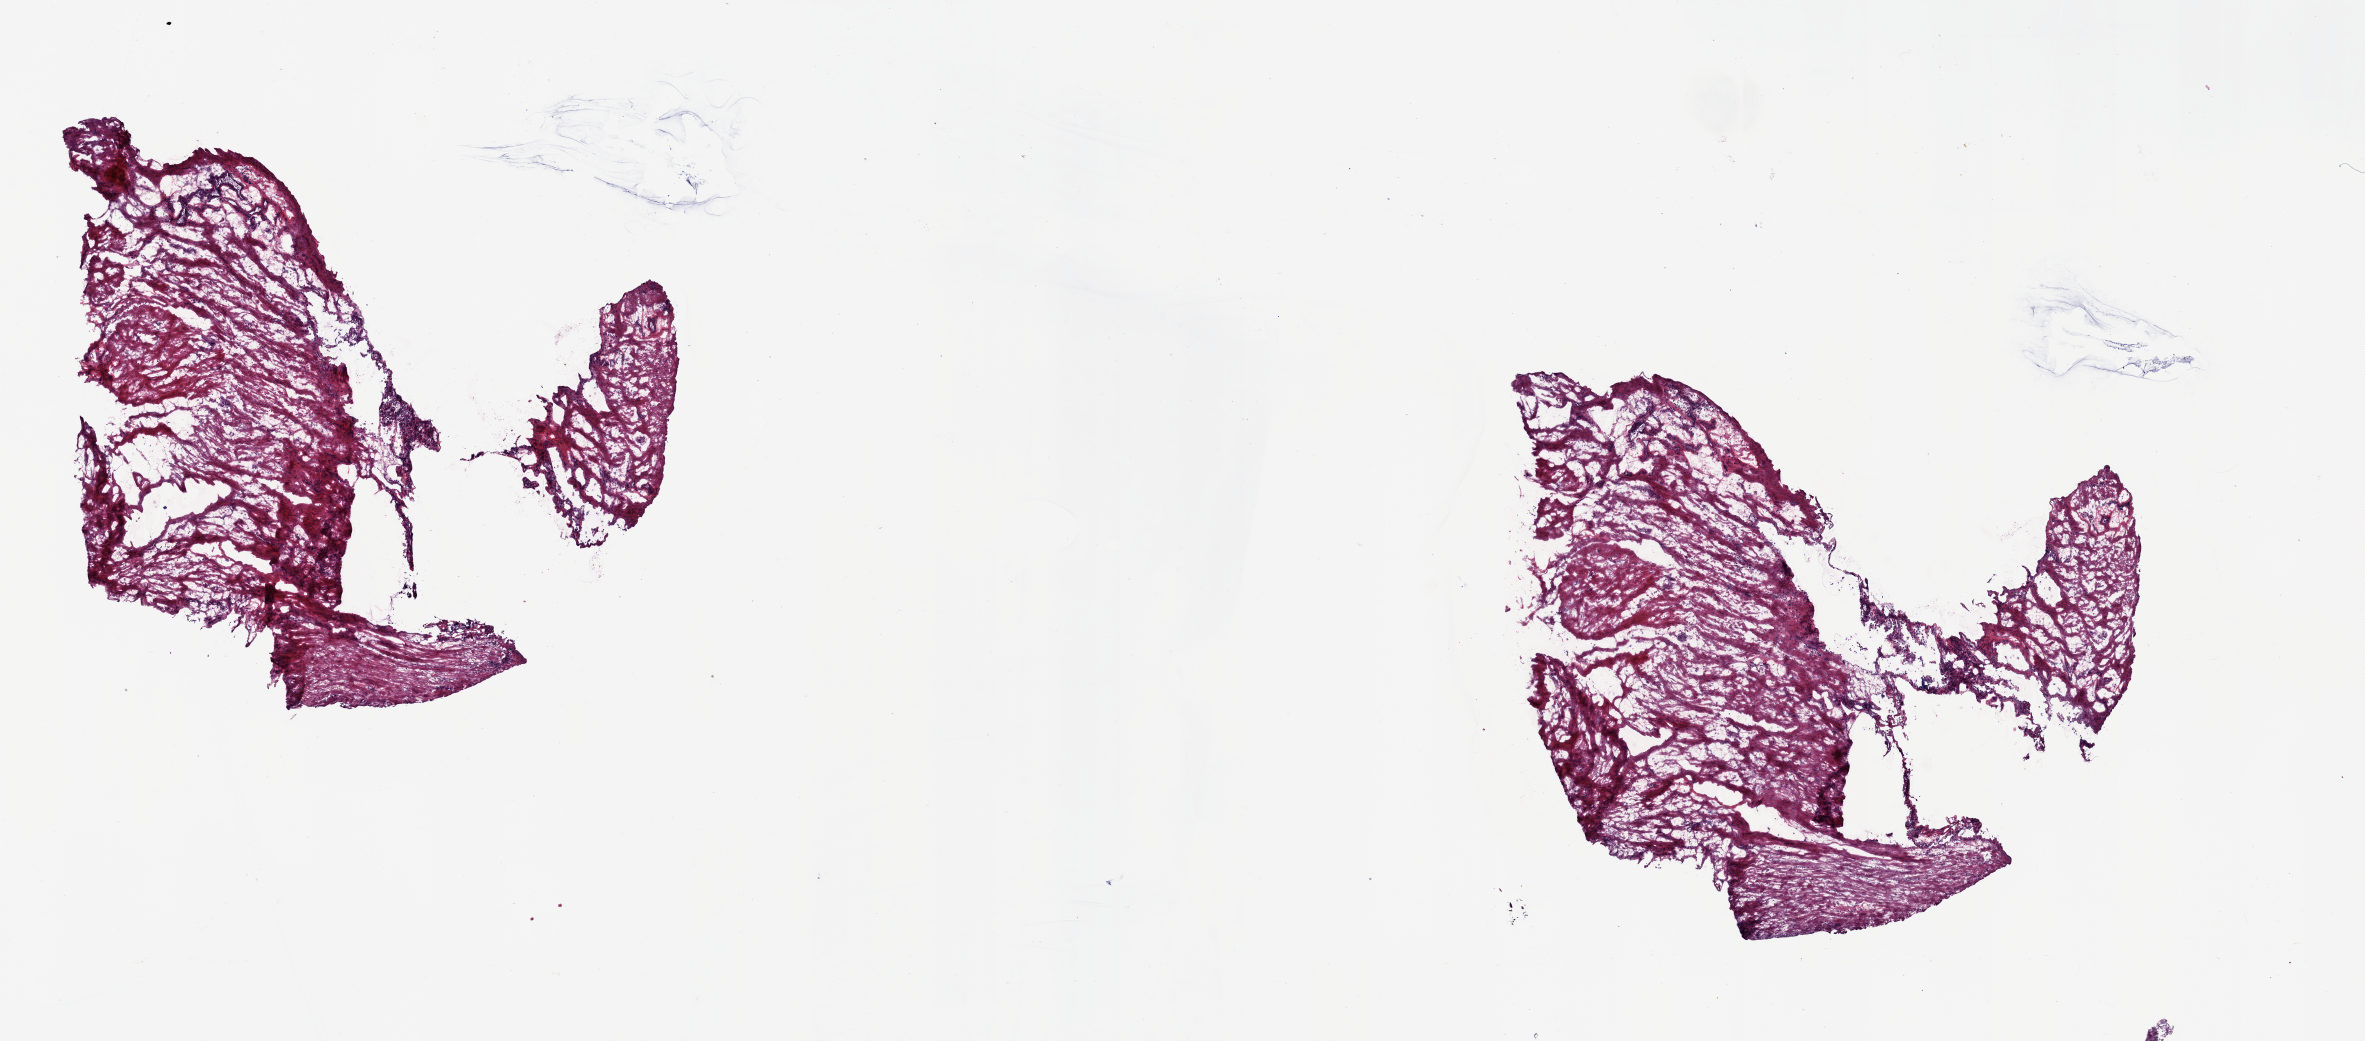
Digitized H&E tissue section (whole slide) — whole scanned area (about 18.6 x 8.2 mm) shown as a low-resolution overview, frozen section, sample: solid tissue normal (non-tumour tissue), stomach. Patient: female, age at initial diagnosis 70 years. Slide review estimates, as recorded: tumour cells 0%, tumour nuclei 0%, normal cells 3%, stromal cells 96%, necrosis 1%. Inflammatory infiltration, as recorded: lymphocyte infiltration 2%, monocyte infiltration 1%, neutrophil infiltration 0%.
This section: solid tissue normal sample (biorepository sample class). Patient diagnosis: Carcinoma, diffuse type (gastric antrum).